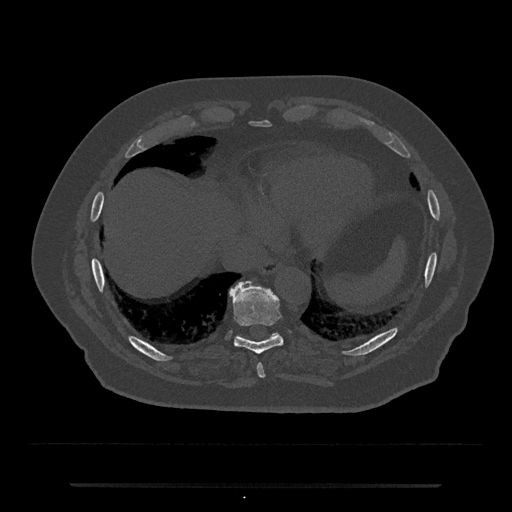
CT including the spine, one axial slice; position 750 of 797 along the scan axis; reconstruction kernel Br40s/3; 120 kVp; bone window (W 1800 / L 400 HU); 0.5 mm slice thickness; 512 × 512 image matrix. Male patient, age 80 years. From the clinical record (not read from this slice): primary cancer: prostate; vertebrae with lytic lesions (as recorded): L1, T11.
Structures marked on this image (semi-automatic segmentation, software-assisted and operator-edited):
- T10 vertebra: bounding box <236,332,279,339> (left, top, right, bottom; pixels)
- T8 vertebra: <257,363,265,378>
- T9 vertebra: <230,281,283,354>